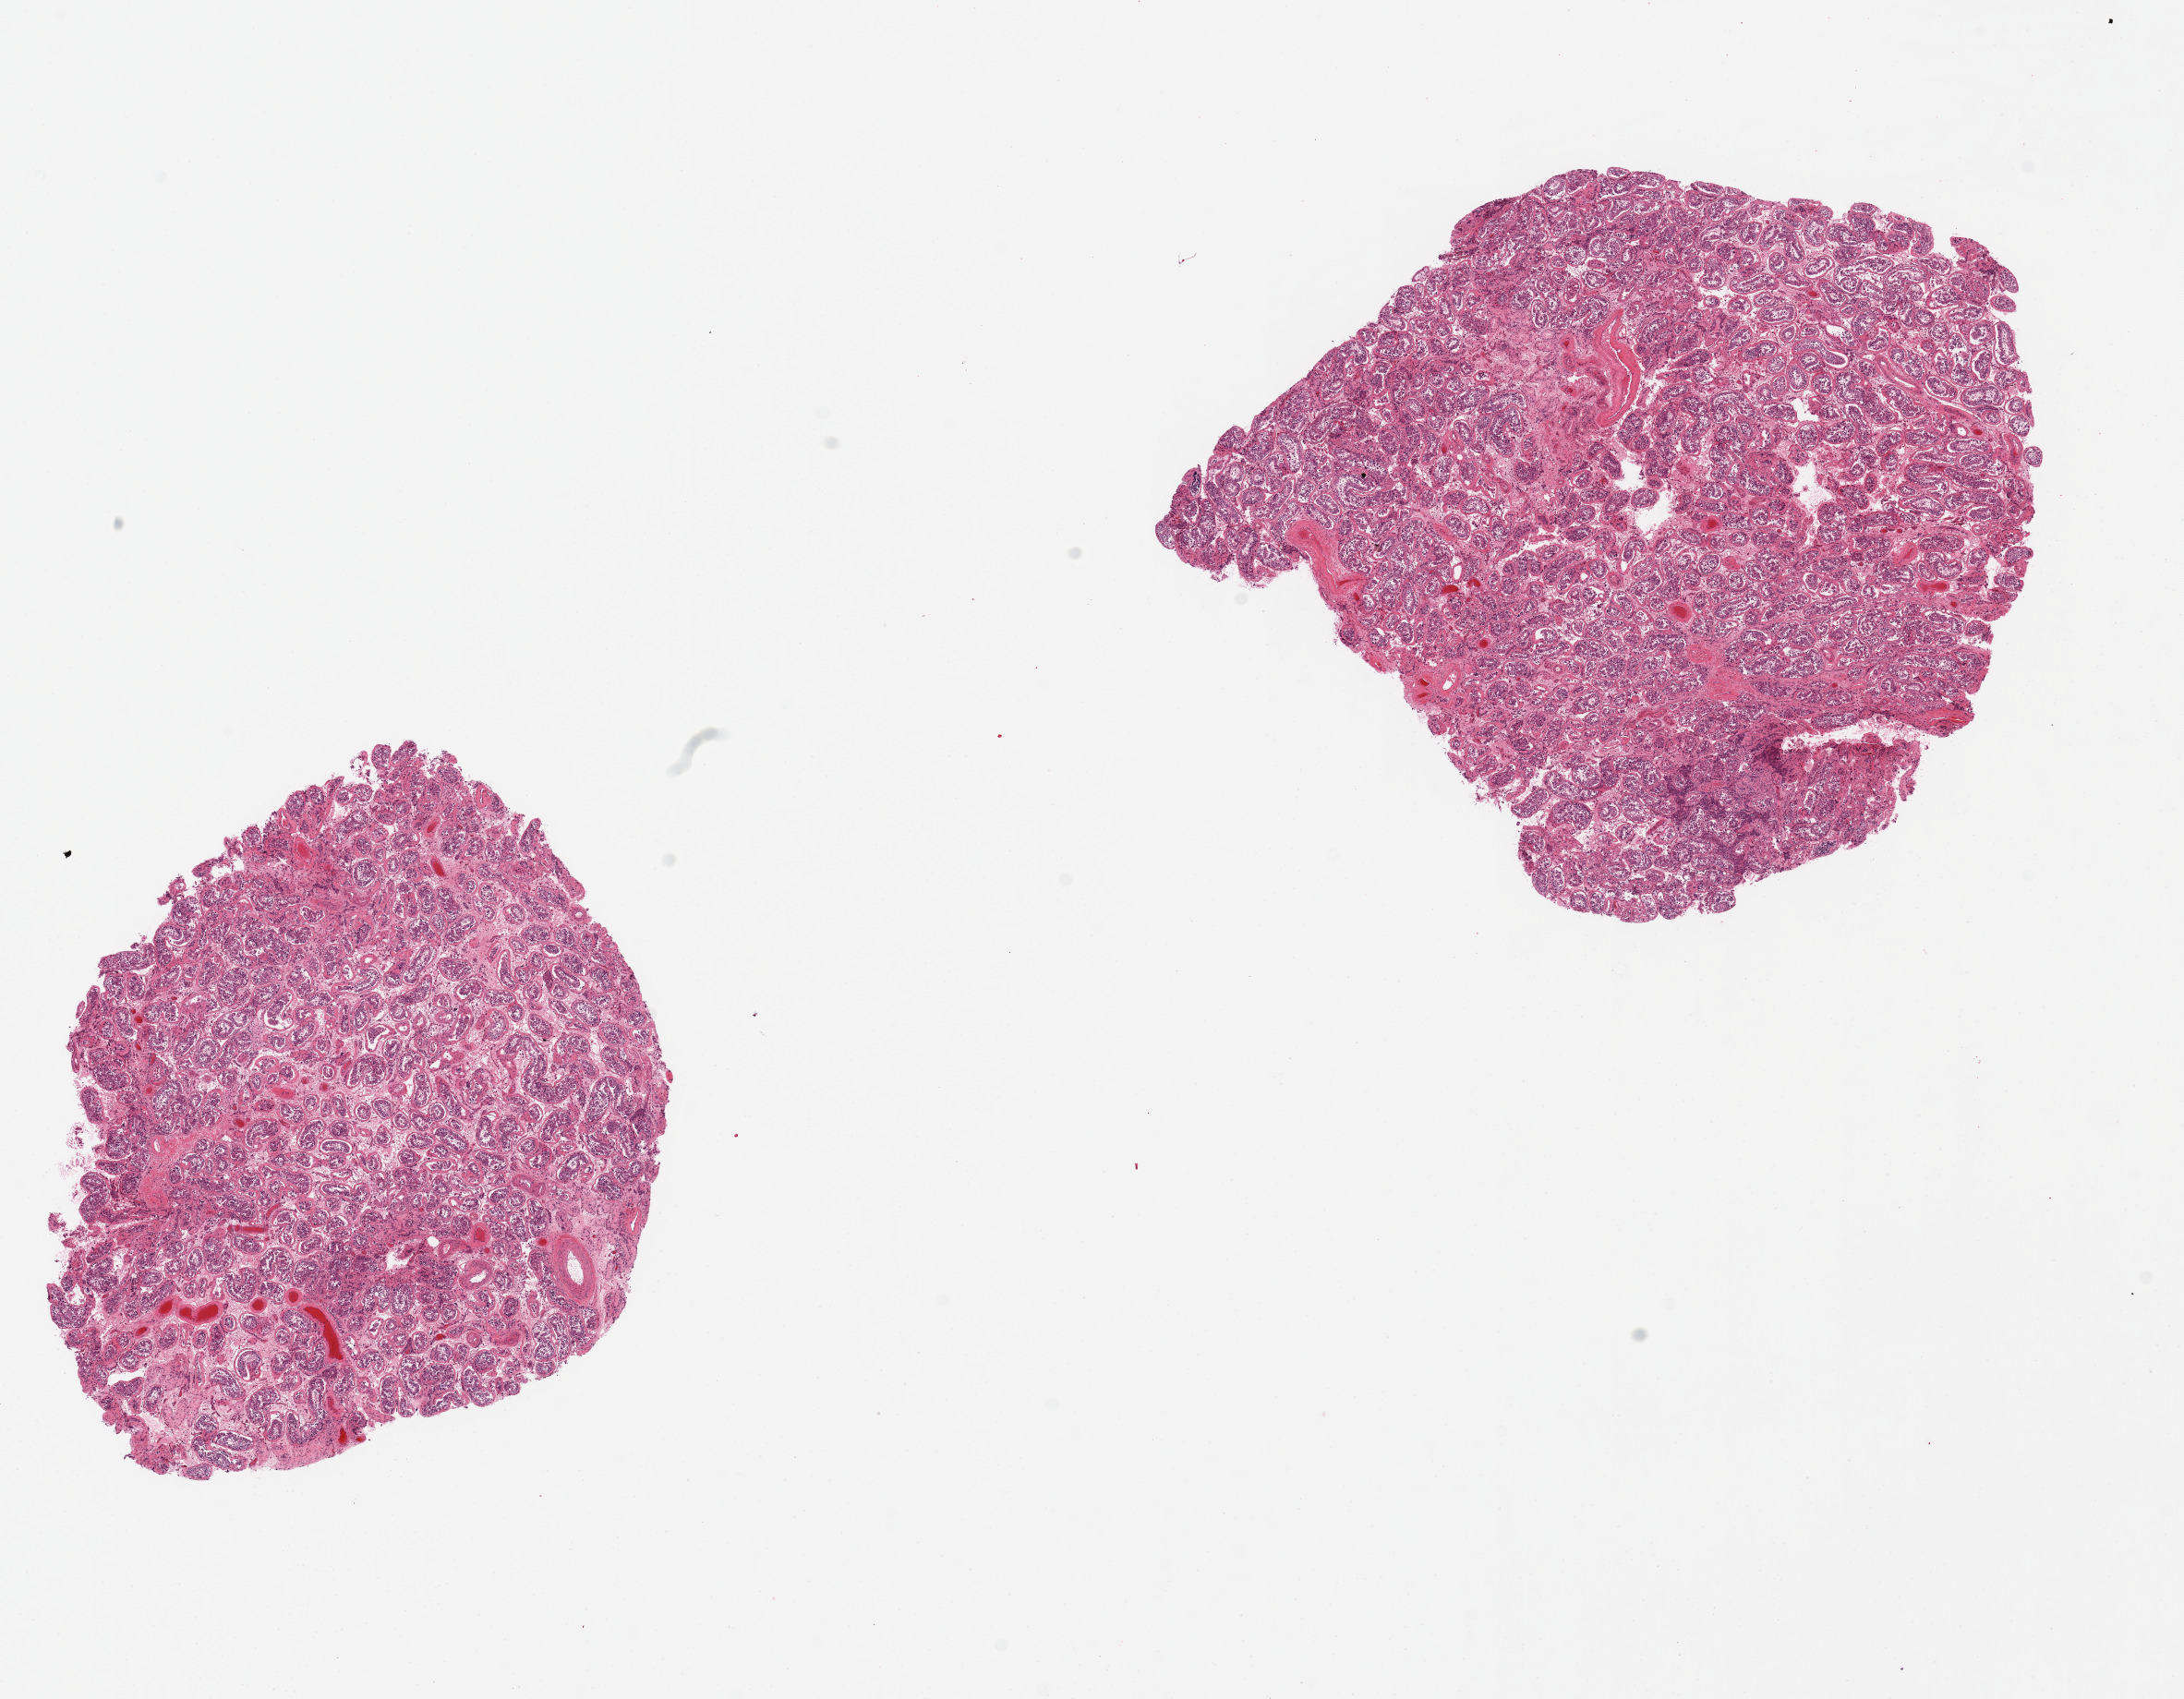
Hematoxylin and eosin (H&E) whole-slide image, low-resolution overview of the scanned area, about 18.7 x 14.6 mm, PAXgene-fixed, paraffin-embedded tissue, sampled site (target tissue): testis, donor tissue sample. Donor: male.
- review note (as recorded): 2 pieces, moderately autolyzed; spermatogenesis is present